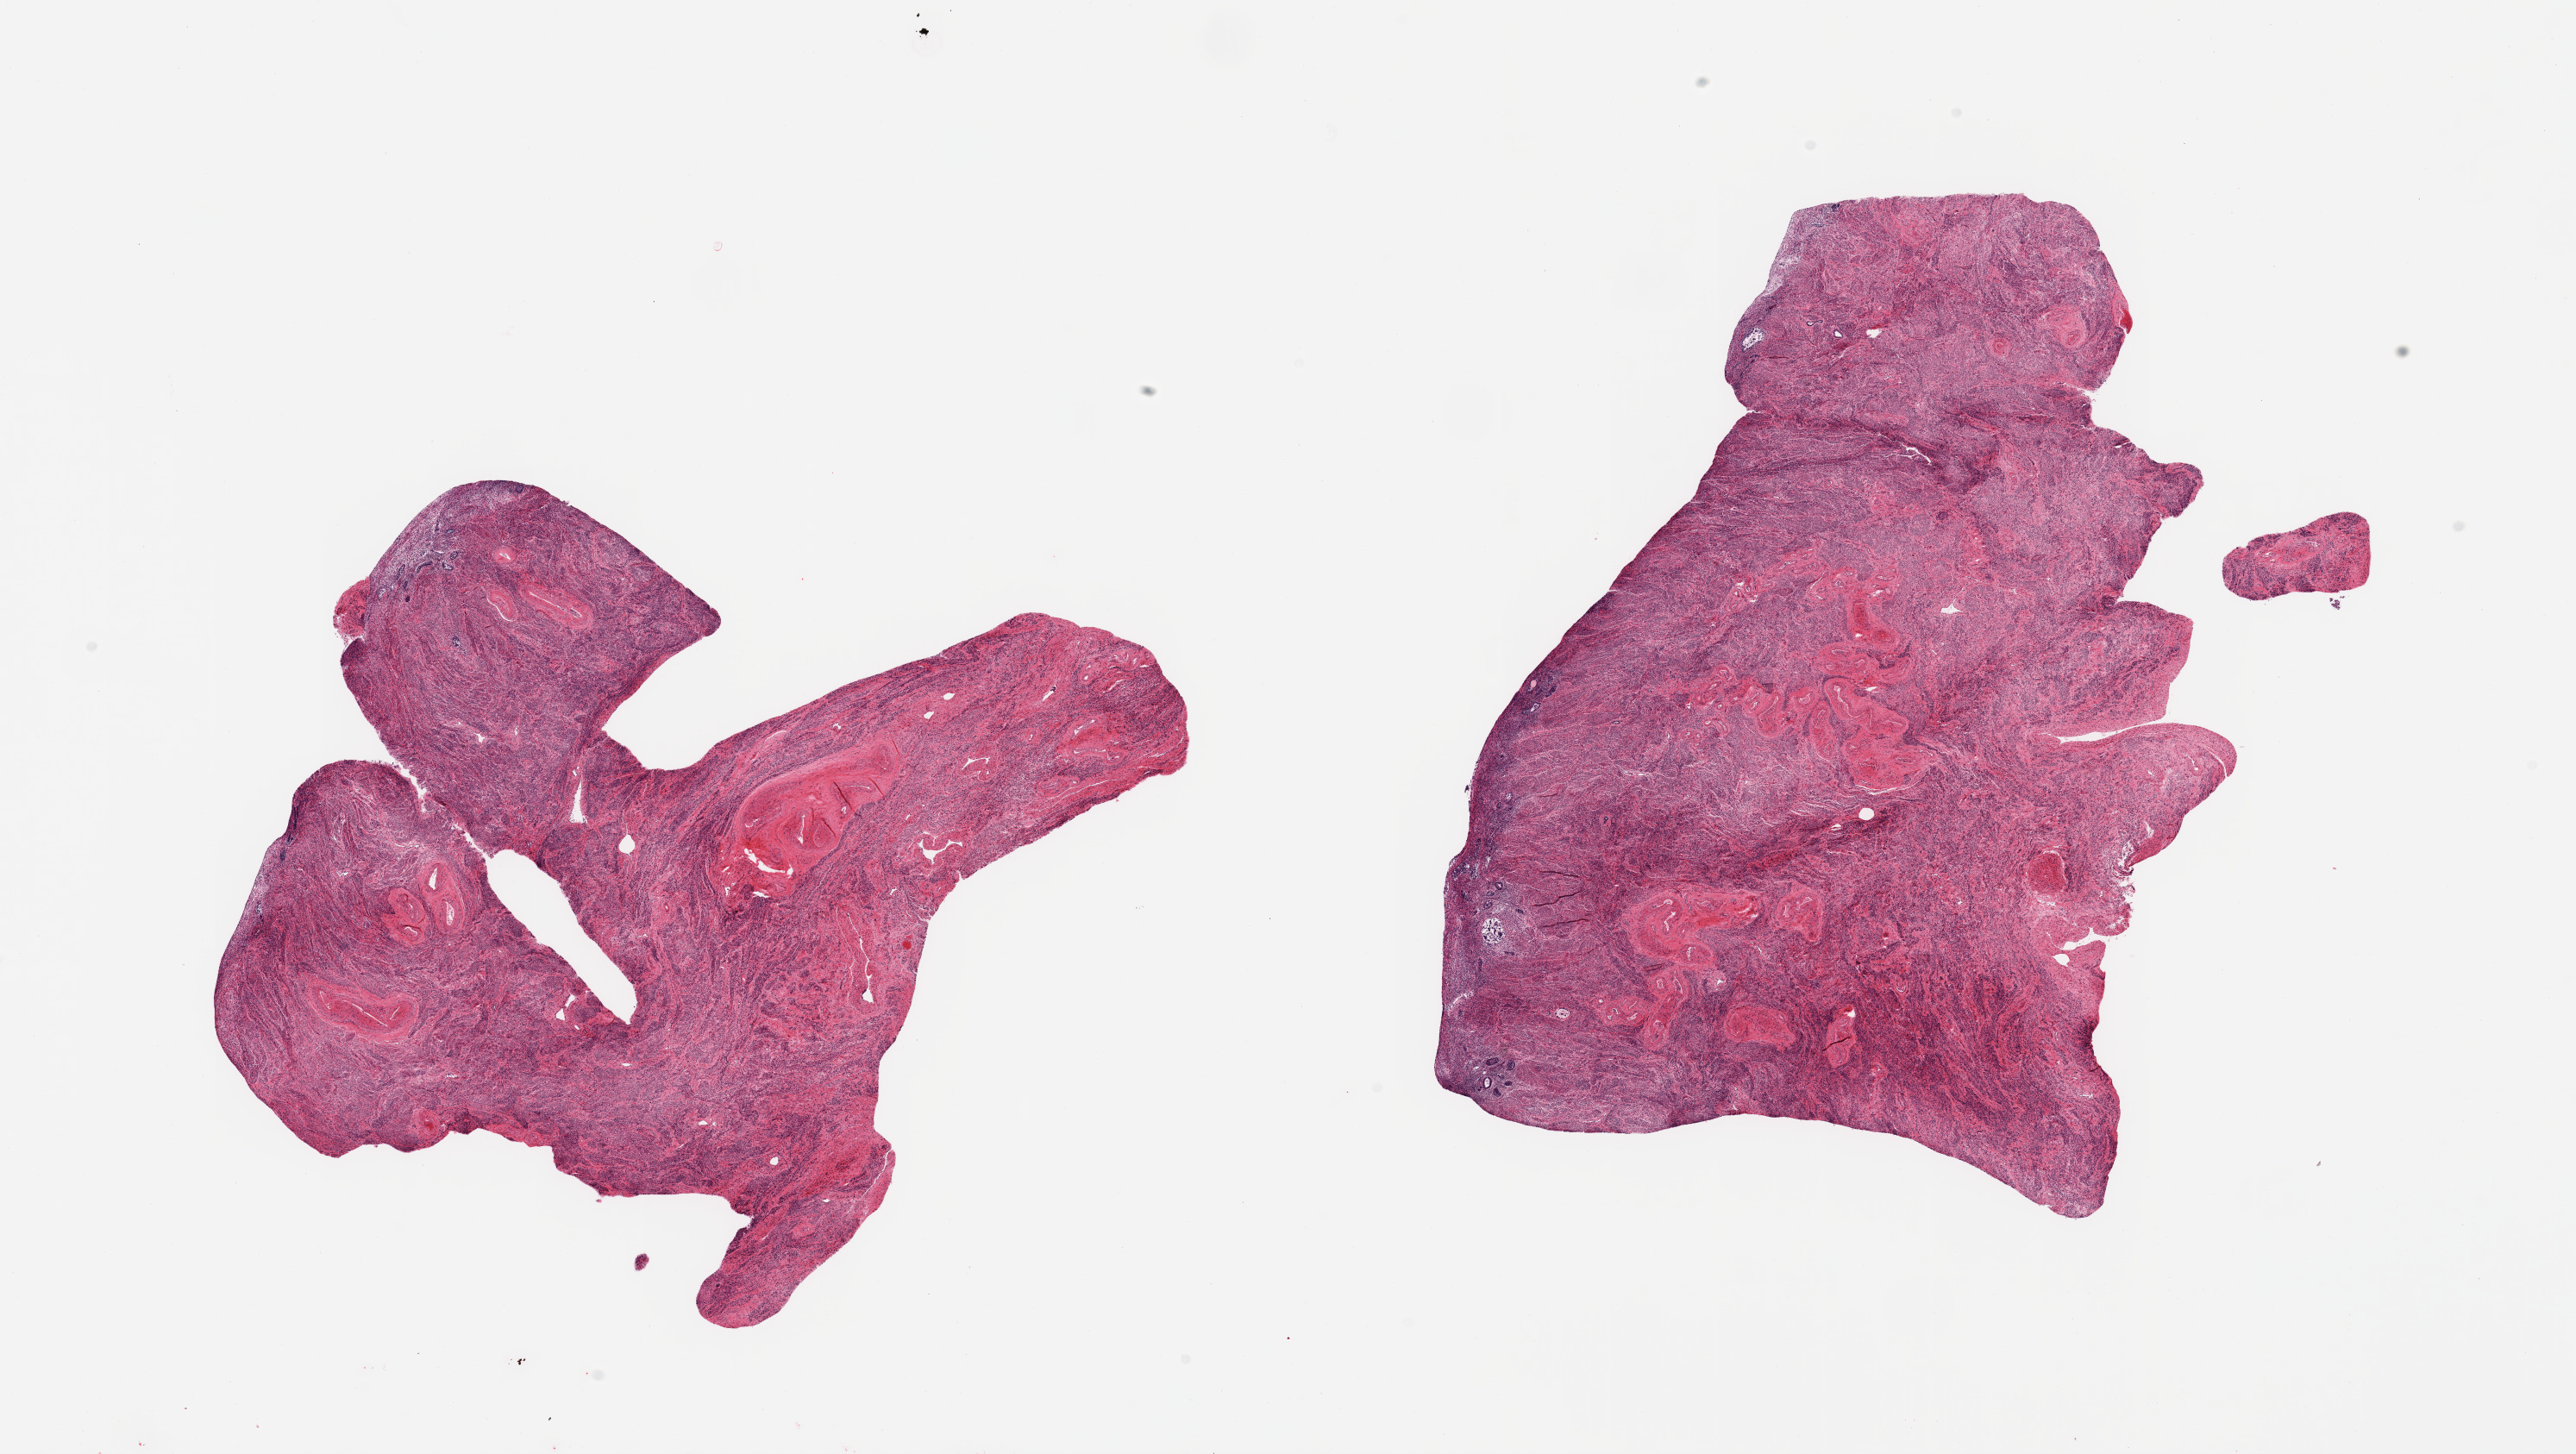
Whole-slide image, haematoxylin and eosin stain, brightfield — a low-resolution overview of the entire scanned area, about 23.6 x 13.3 mm (from a 20x scan). PAXgene-fixed paraffin-embedded (PFPE) section. Section of uterus (target tissue). Donor tissue sample.
Pathologist's review note for this sample: 2 pieces; atrophic & autolyzed endometrium.